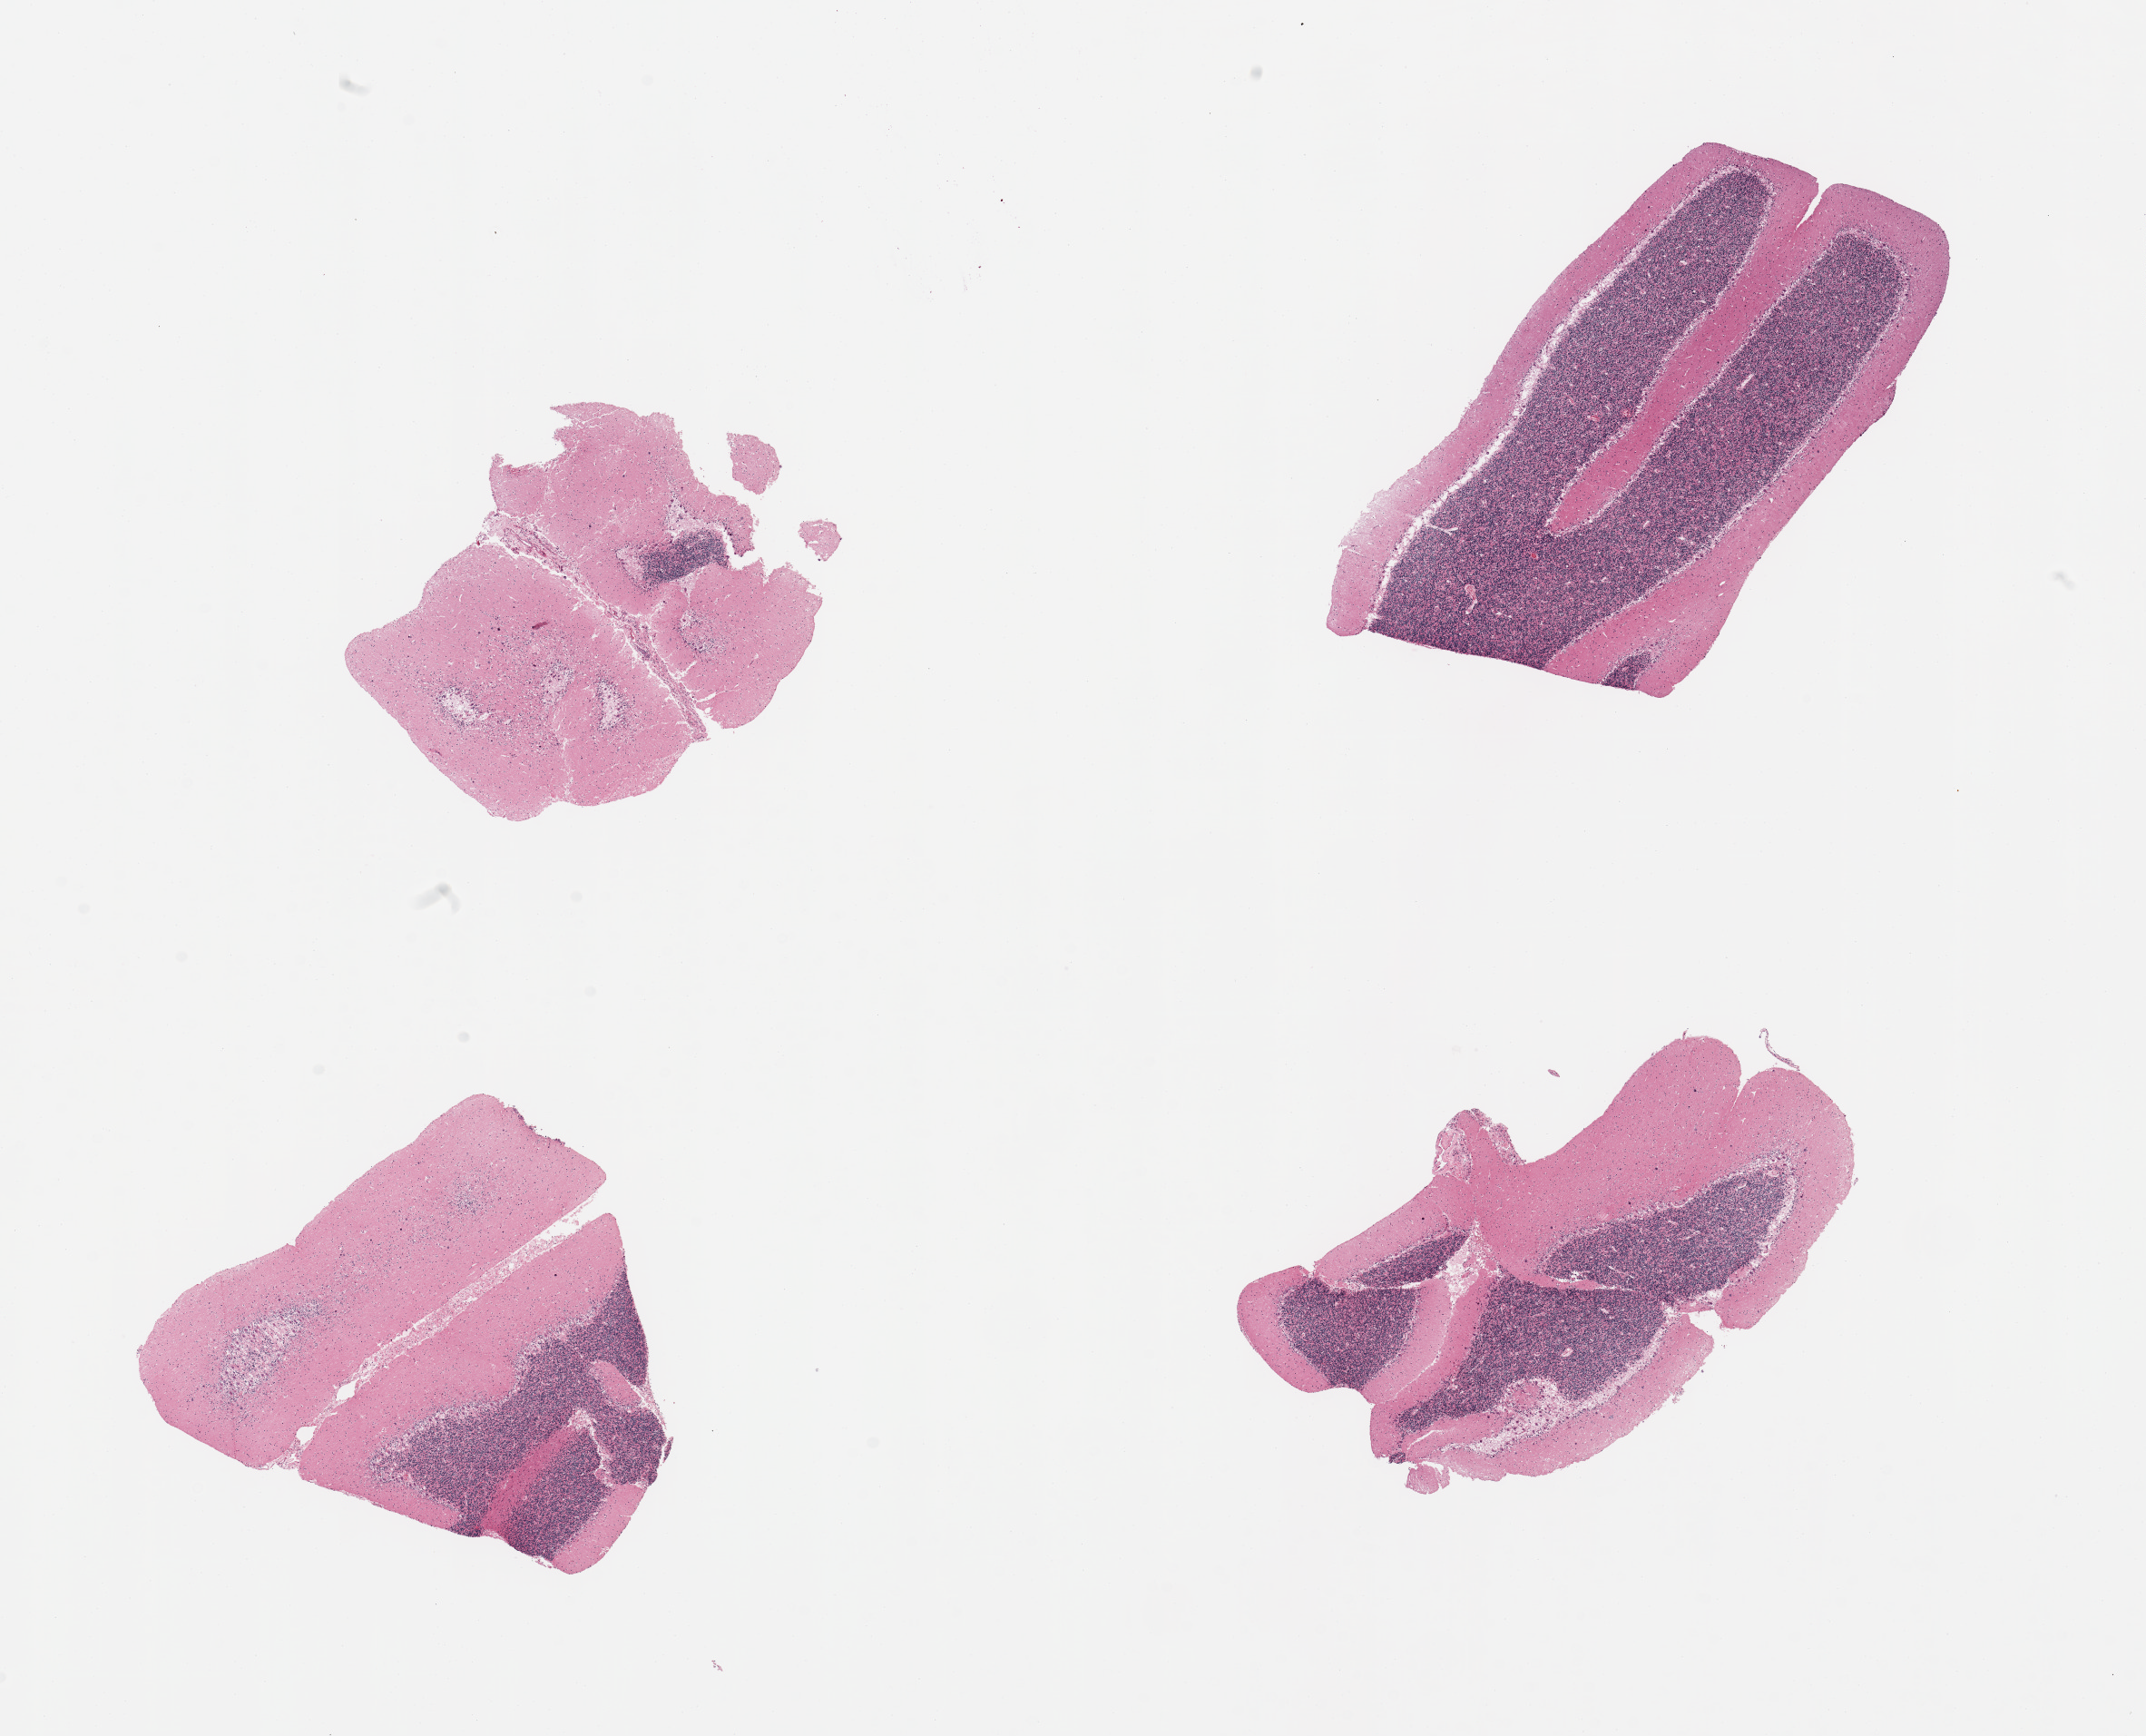
Haematoxylin and eosin whole-slide image — whole scanned area (about 18.7 x 15.1 mm) shown as a low-resolution overview; PAXgene-fixed paraffin-embedded (PFPE) section; section of cerebellum (target tissue); tissue donor sample. Donor: male.
* review note (as recorded): 4 pieces